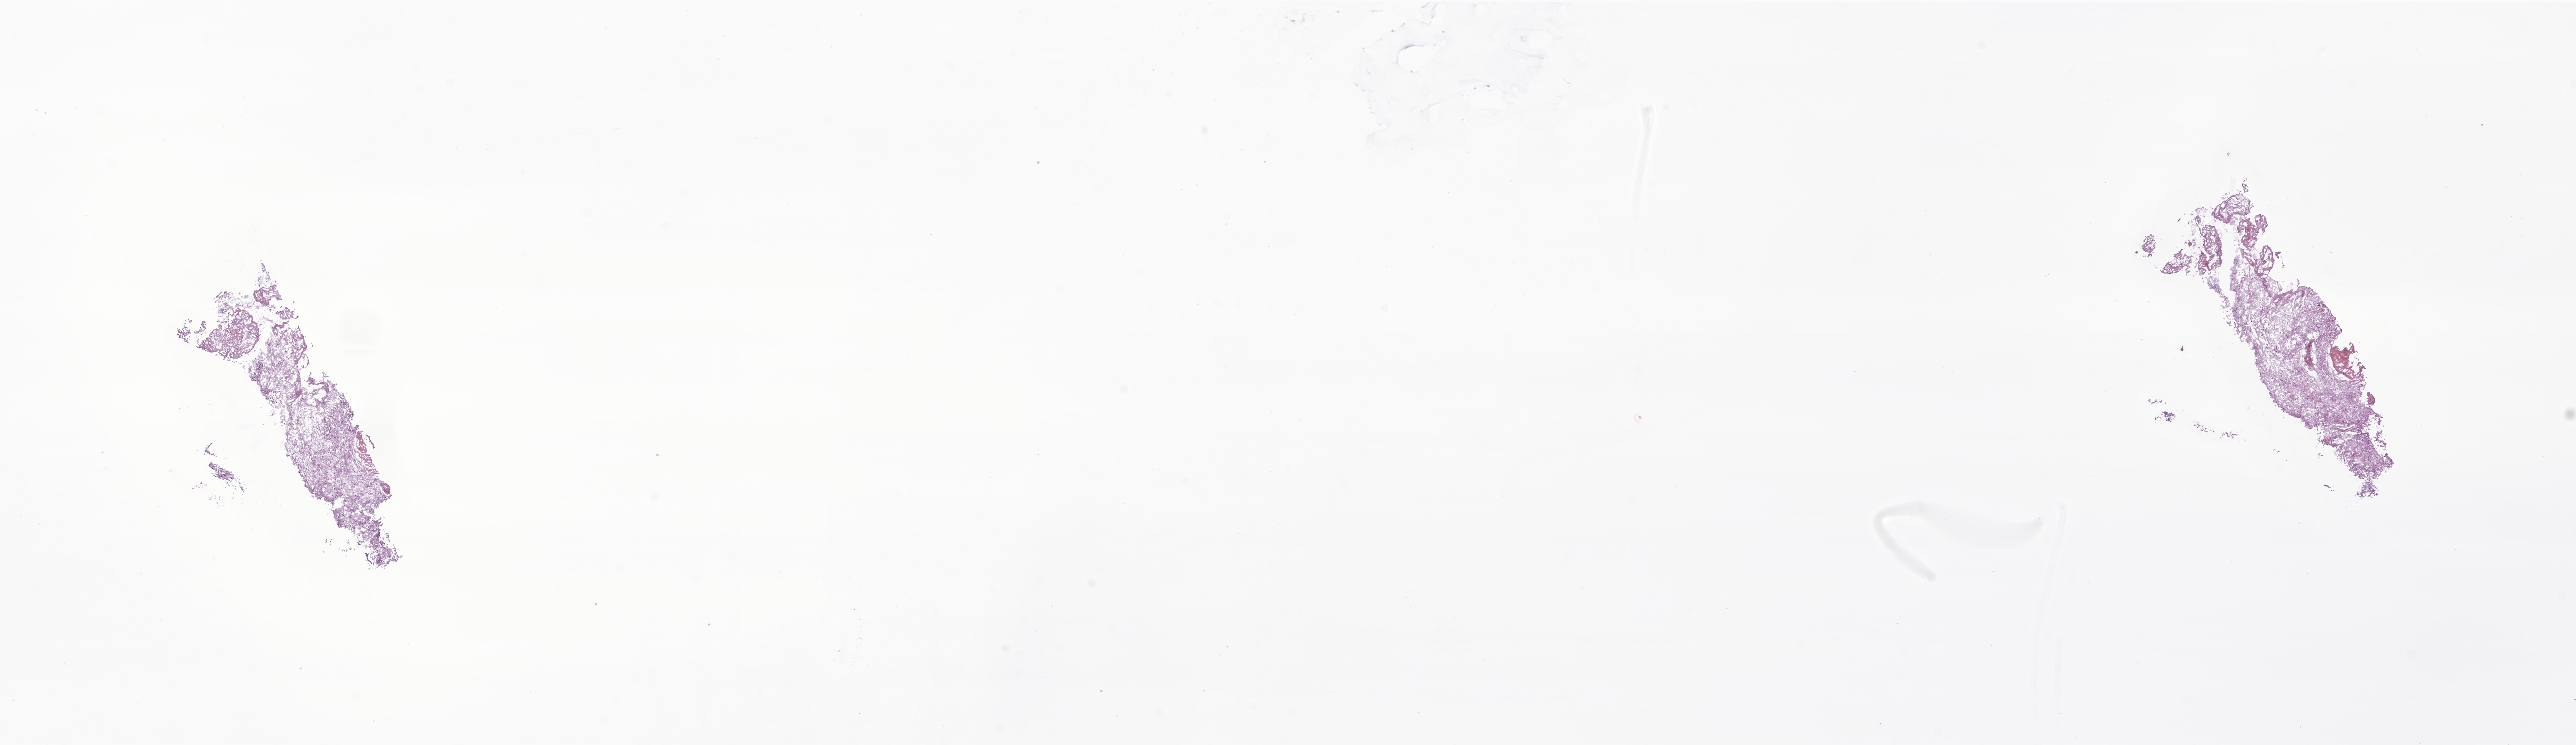
Whole-slide image, hematoxylin and eosin (H&E) stain of tumor tissue from the brain — a low-resolution overview of the entire scanned area, about 27.7 x 8.0 mm, cryosection (OCT / tissue freezing medium). Patient: female, age 142 months (11 years 10 months).
Diagnosis: Pilocytic astrocytoma.